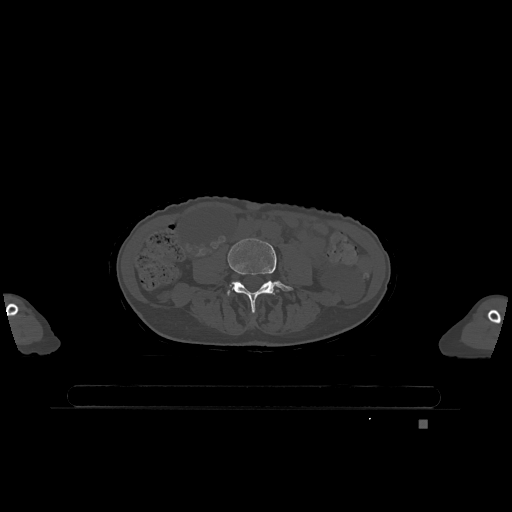
CT including the spine, one axial slice. Position 295 of 1317 along the scan axis. Bone window (W 1800 / L 400 HU). 0.5 mm slice thickness. 512 × 512 image matrix. Patient: female, 74 years. From the clinical record (not read from this slice): primary cancer: lung; vertebrae with lytic lesions (as recorded): T1, T4, T5, T6, L4, L5.
Annotated regions visible in this slice (semi-automatic segmentation, software-assisted and operator-edited):
- L4 vertebra: bounding box <228,238,293,312> (left, top, right, bottom; pixels)